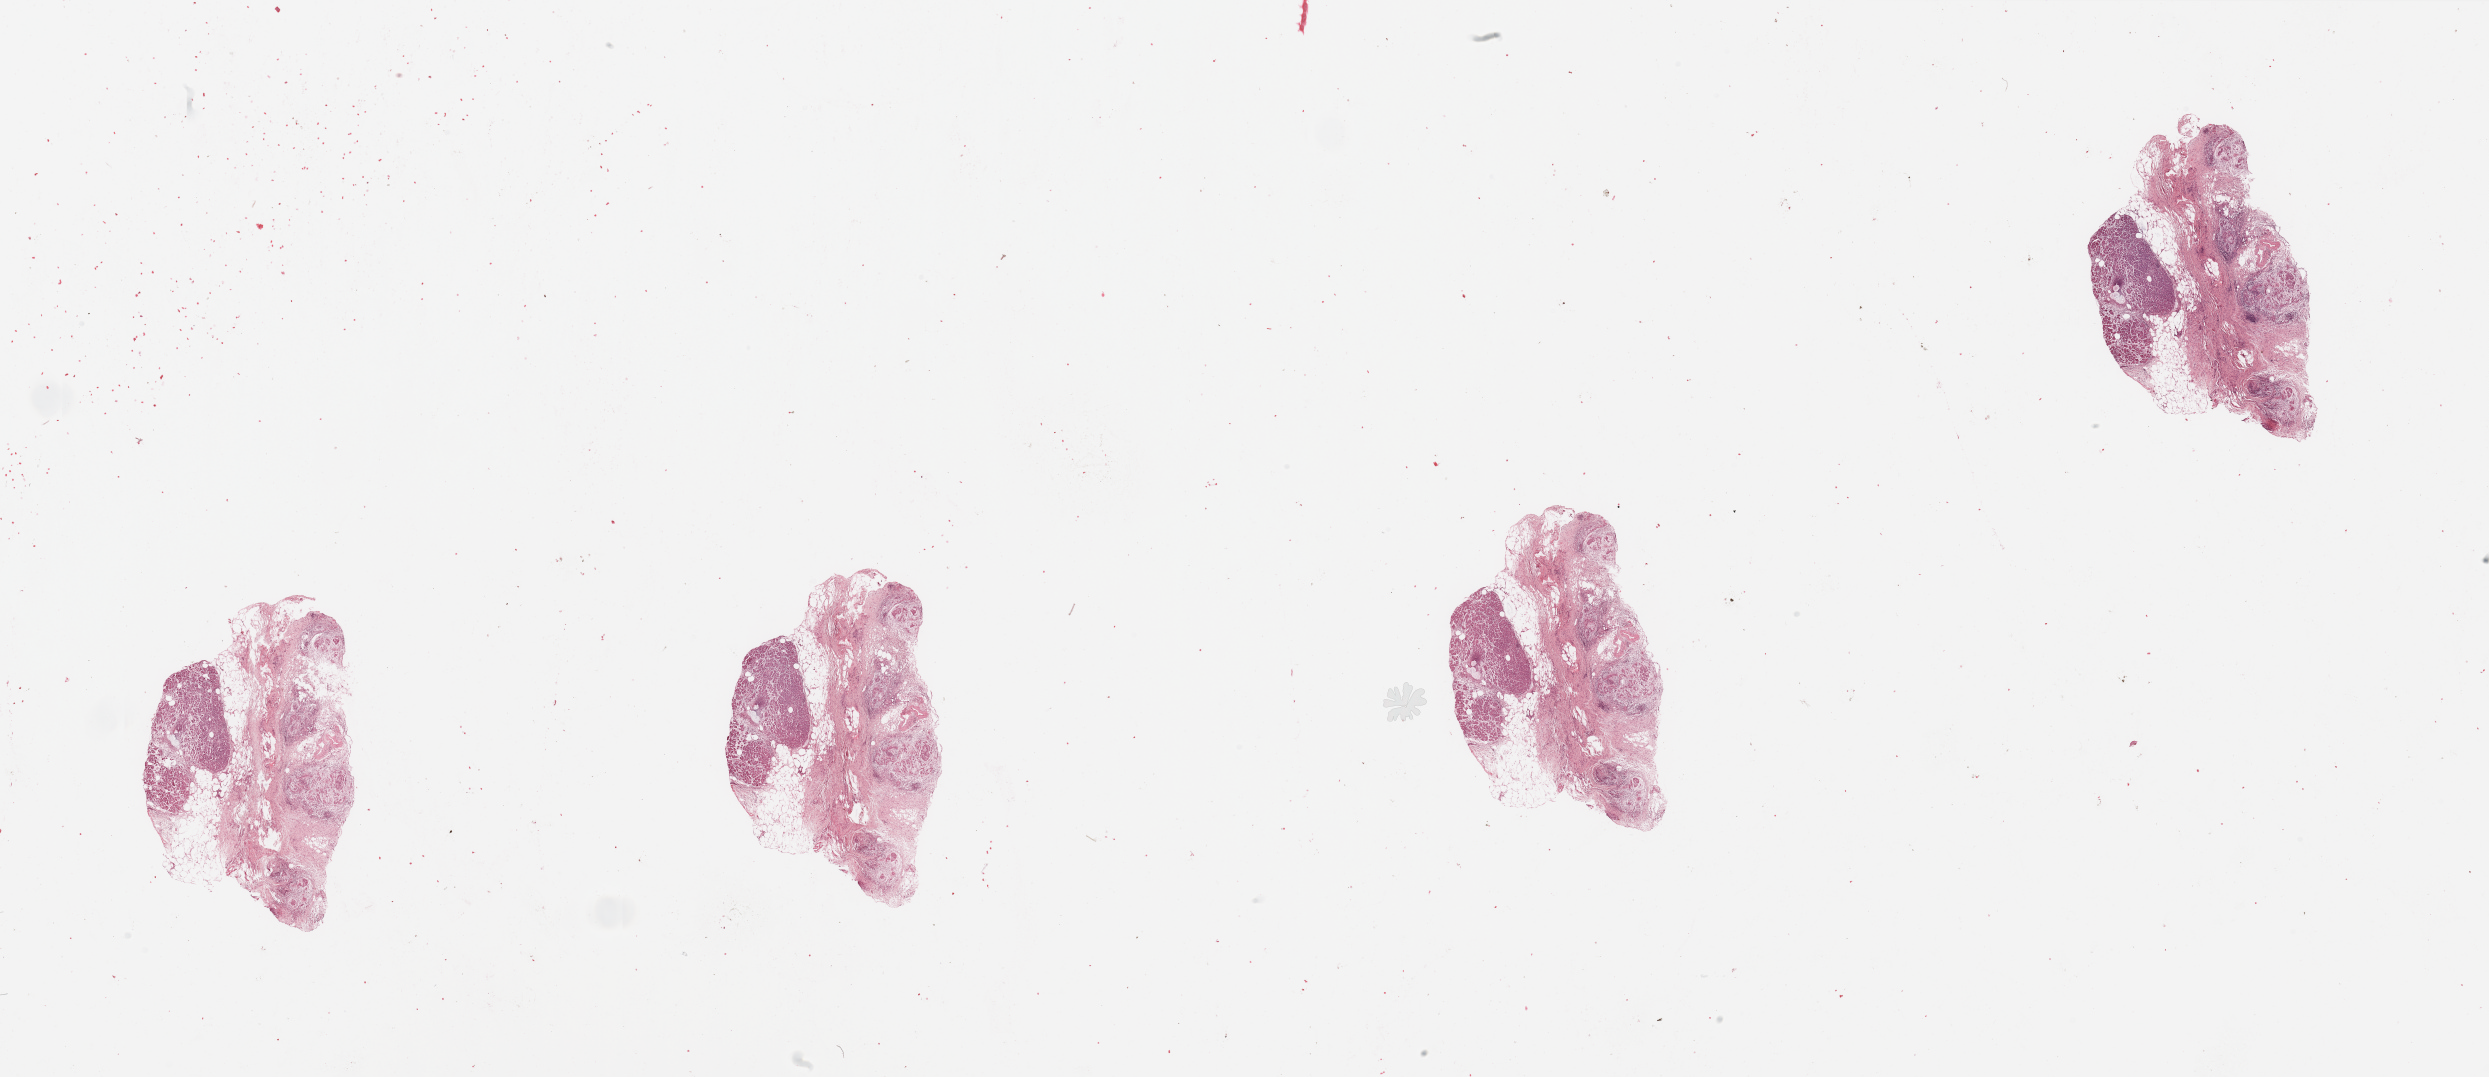
Digitized H&E-stained tissue section (whole slide), low-resolution overview of the scanned area, about 39.4 x 17.0 mm (acquisition: 20x scan). Normal (non-tumour) tissue sample, pancreas. Patient: female, age 68 years.
This section: normal (non-tumour) tissue from the same patient. Patient diagnosis: Infiltrating duct carcinoma, NOS.